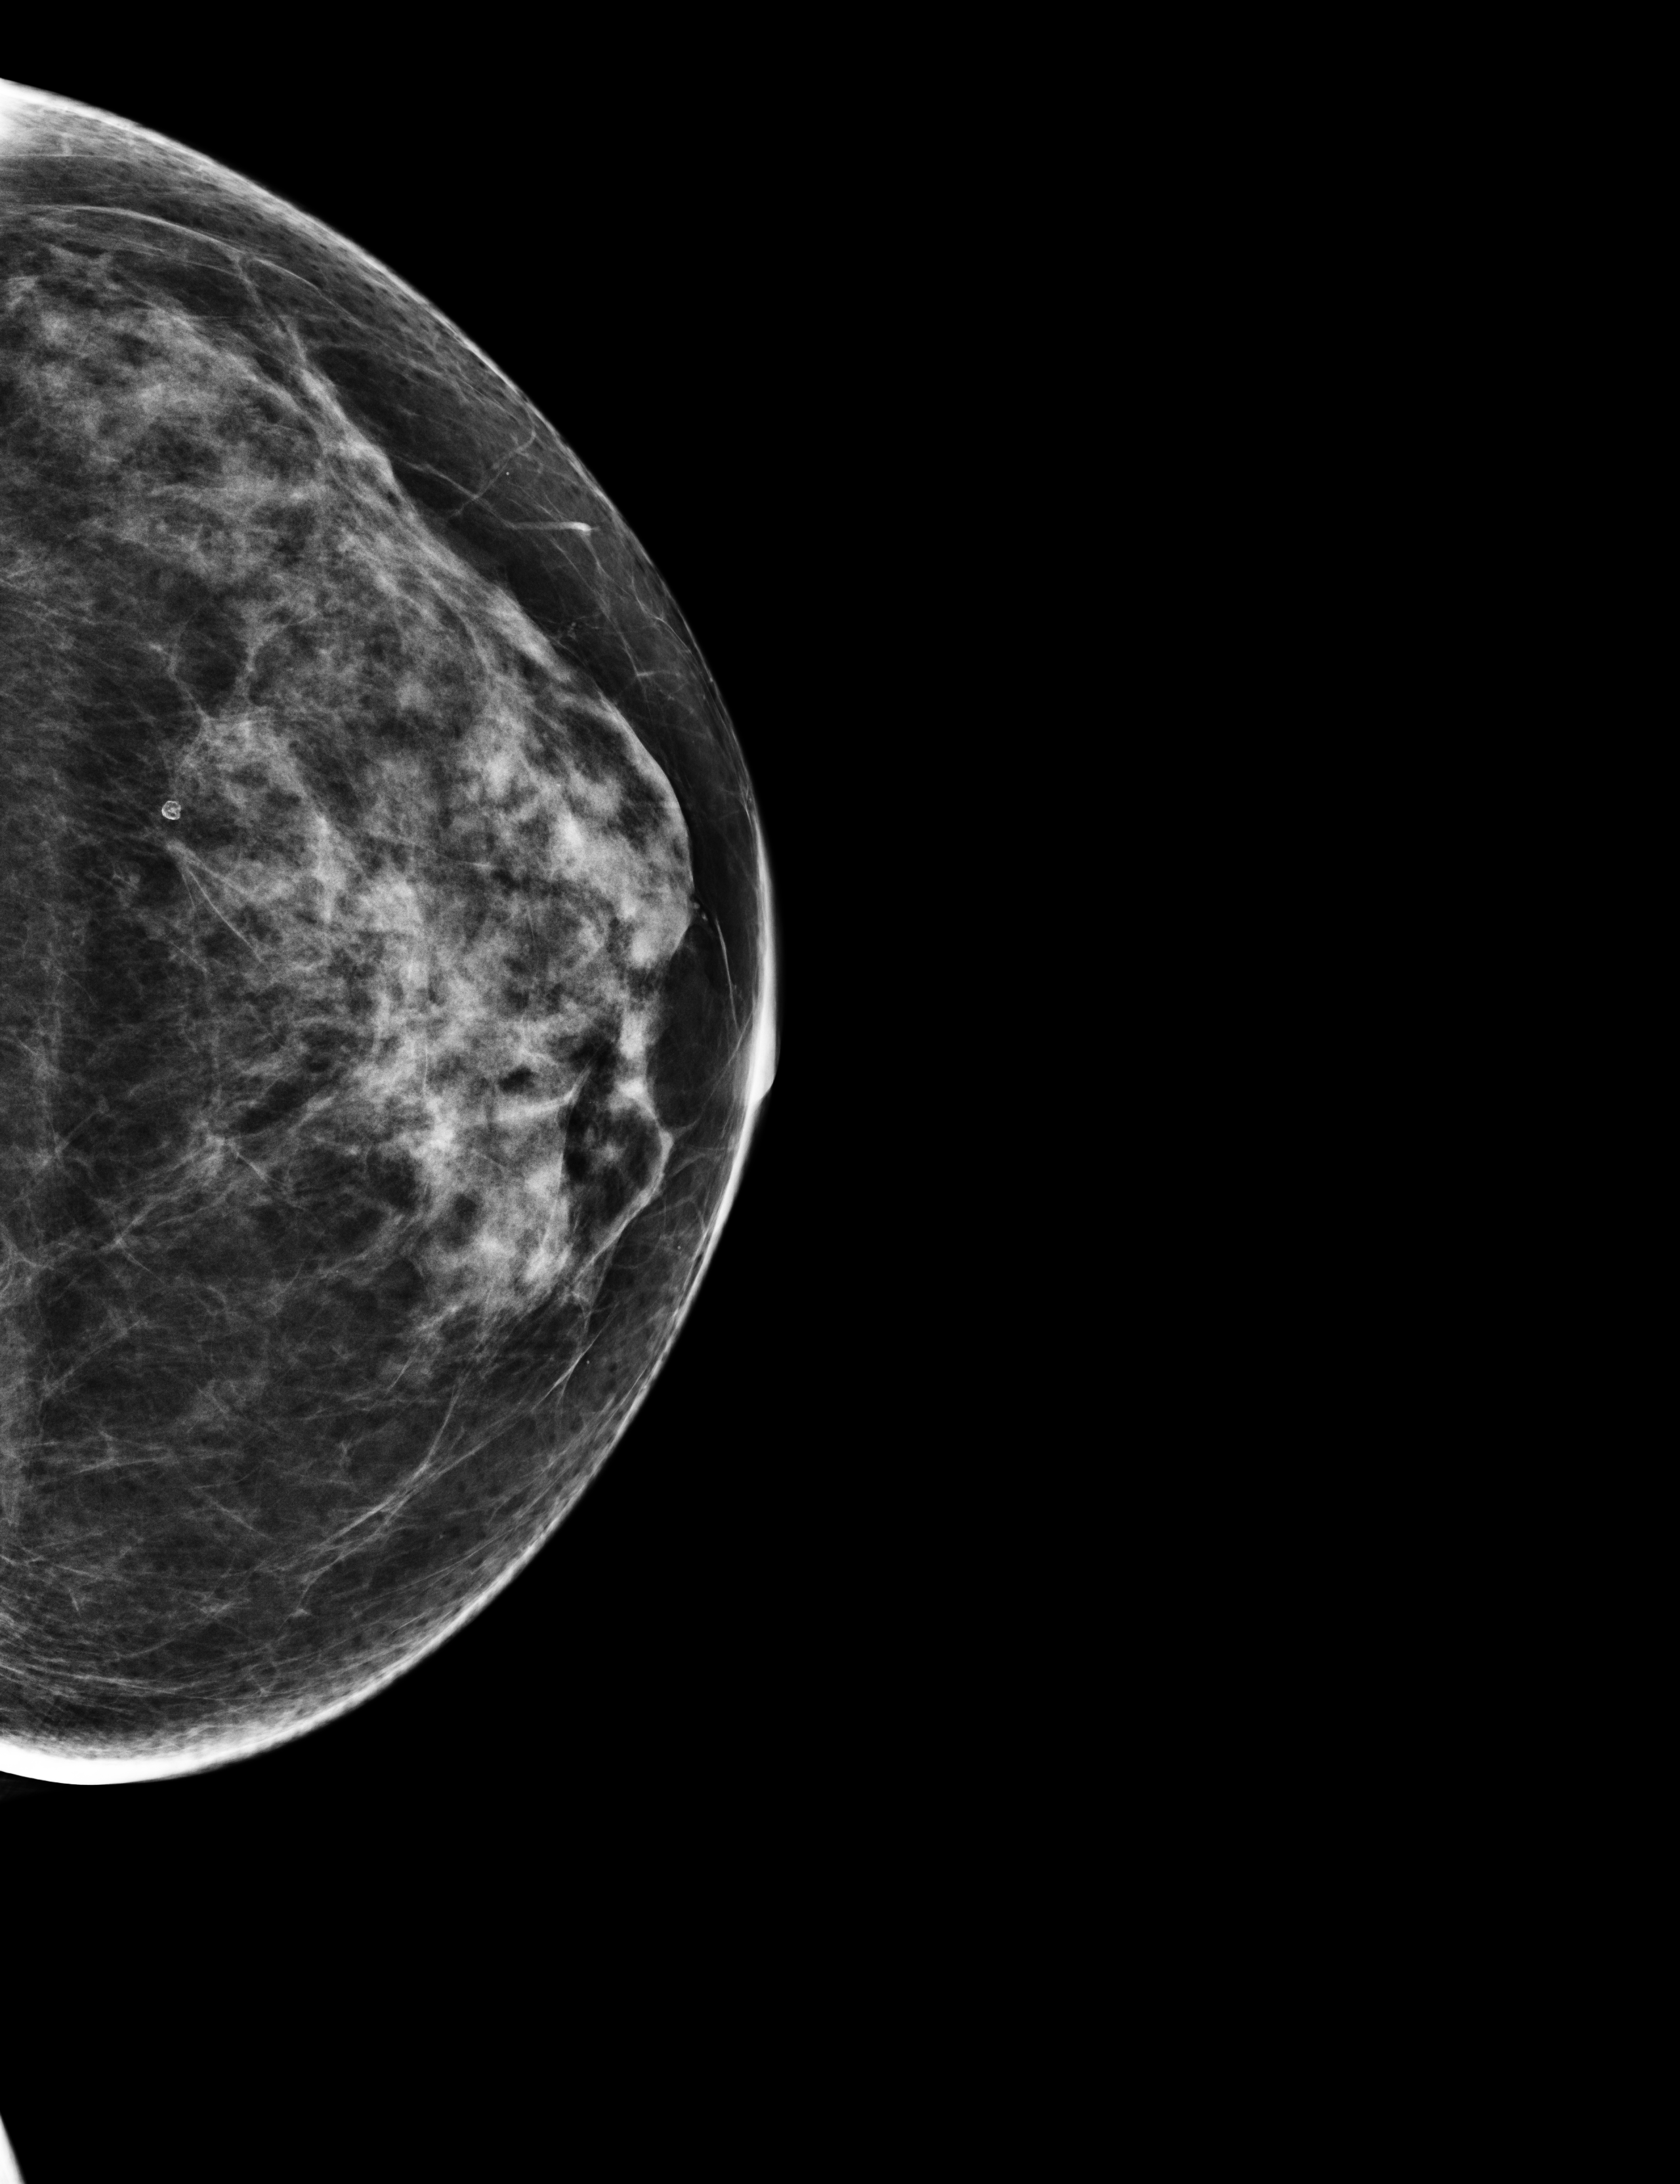
Annual screening mammography examination, system: Selenia Dimensions.
Image type: full-field digital mammogram. Breast: left. Projection: cranio-caudal projection.